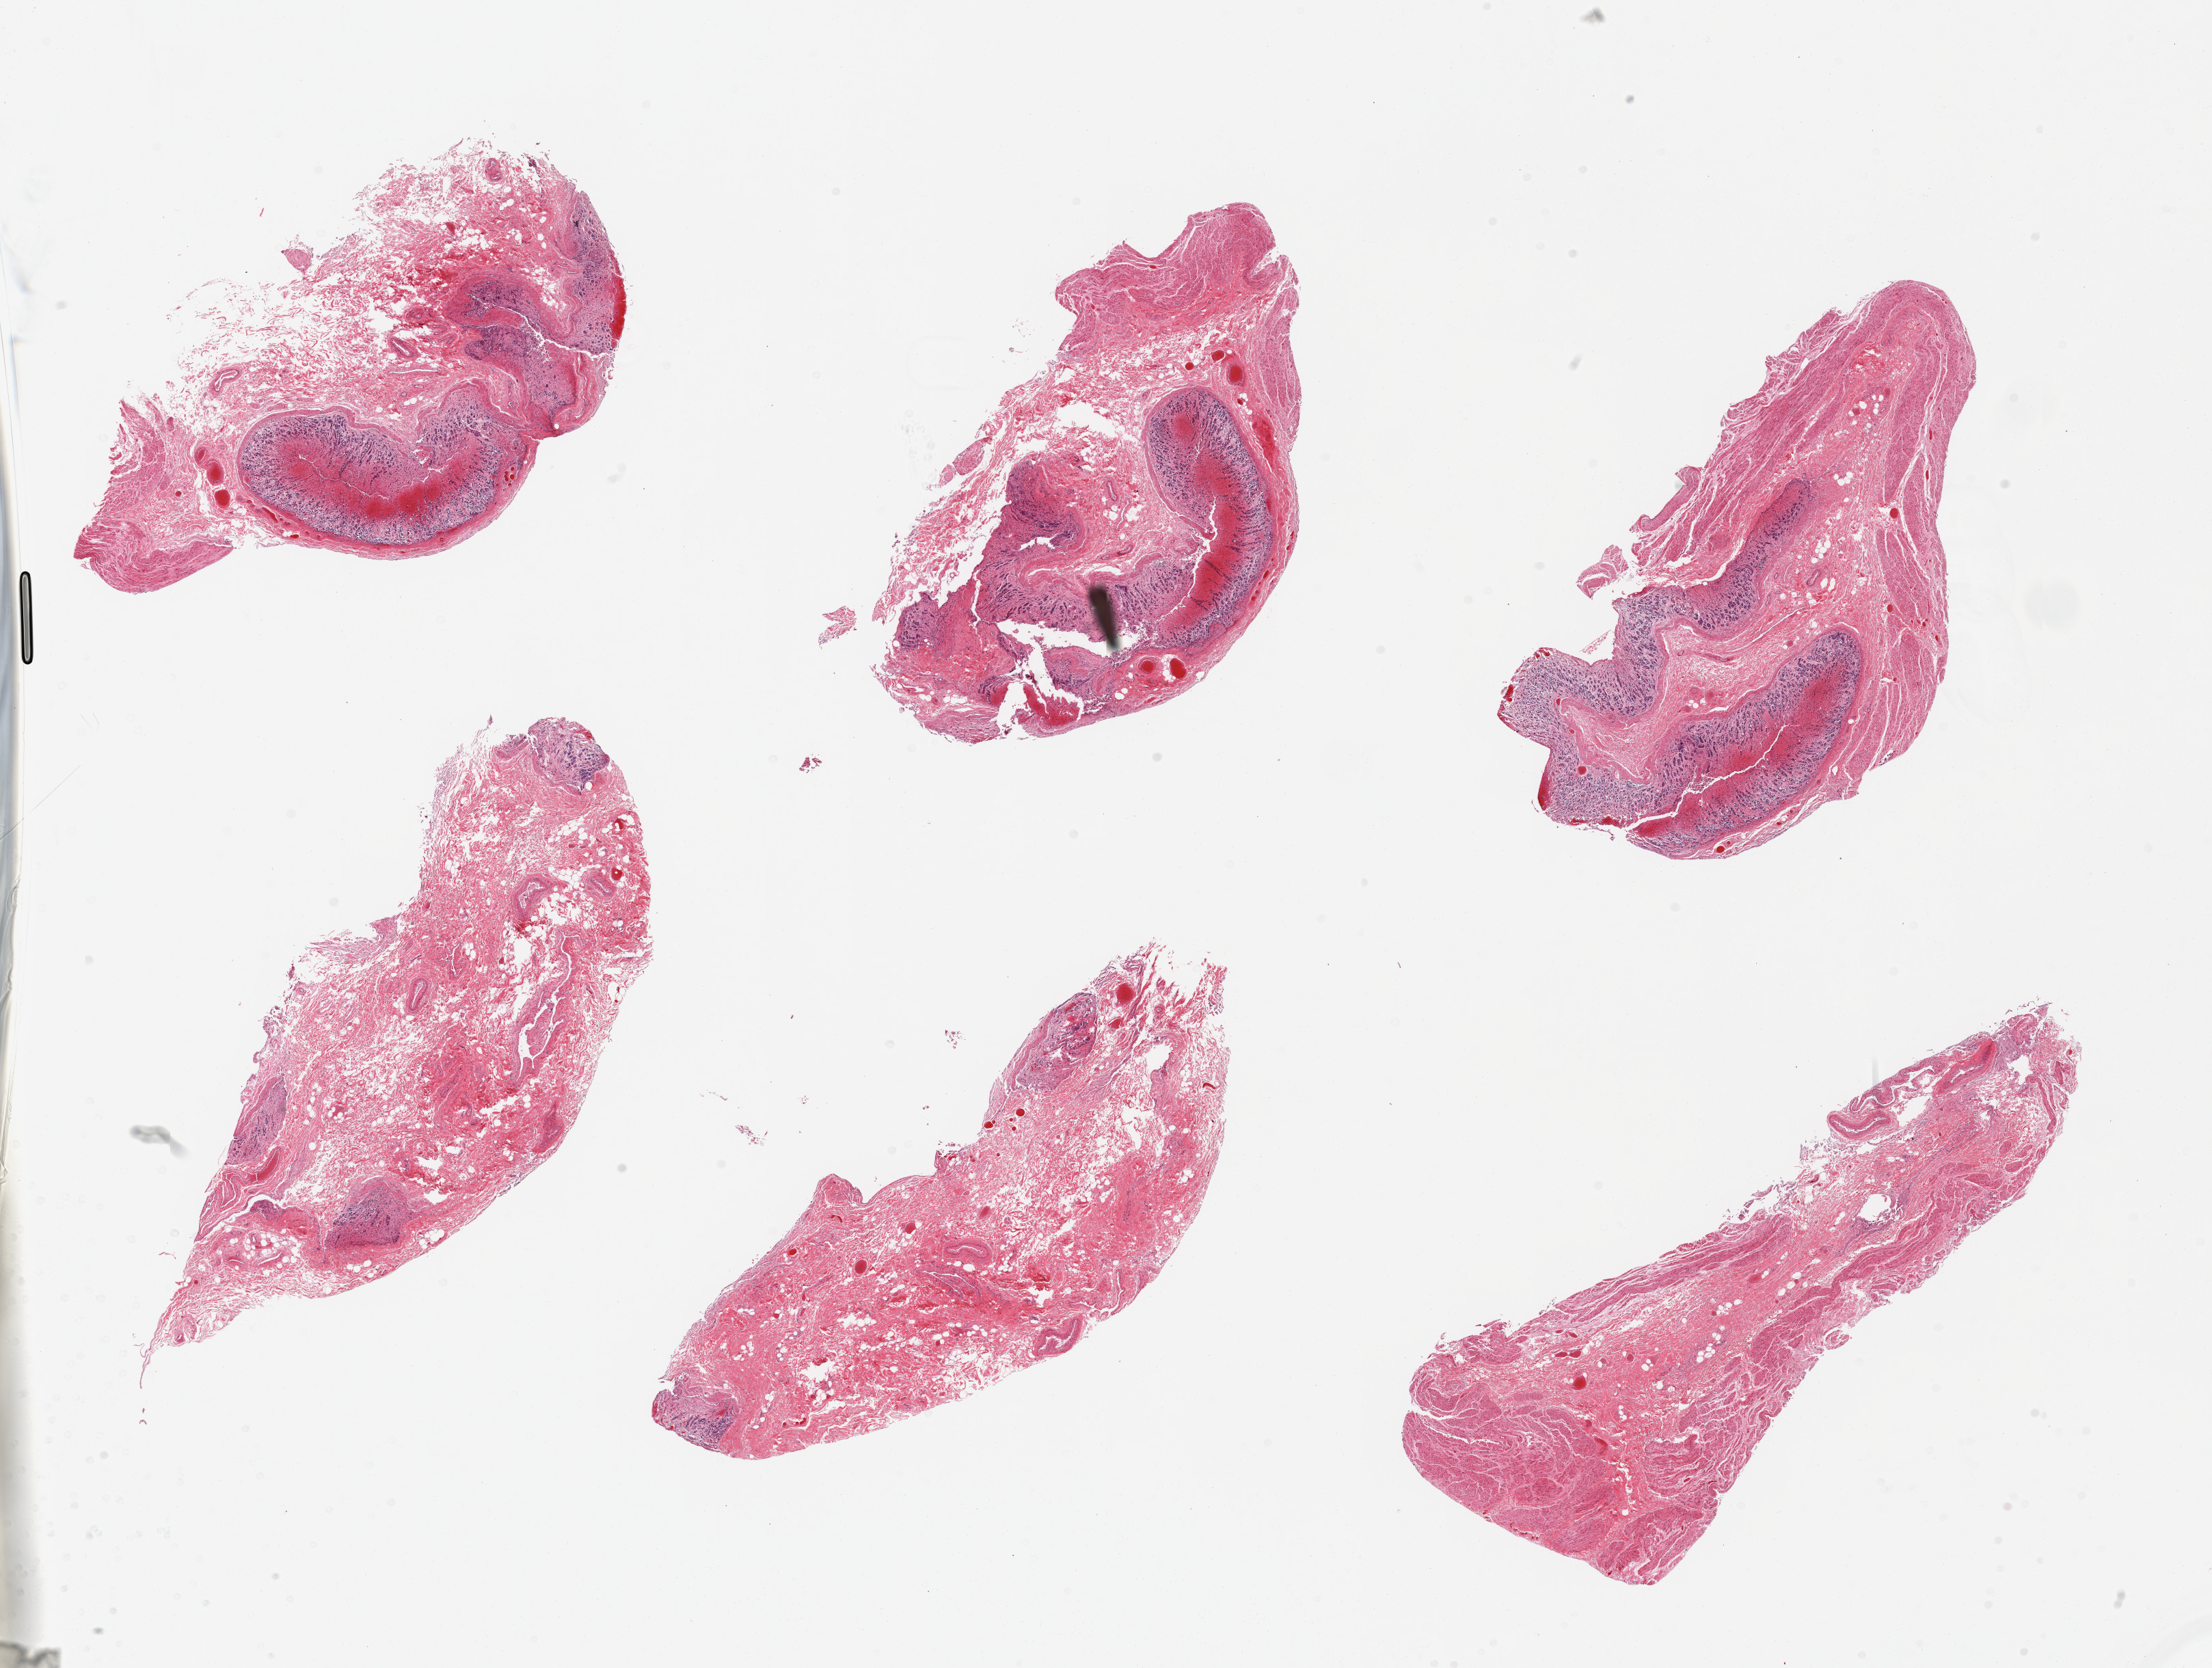
Digitized haematoxylin and eosin-stained section, a low-resolution overview of the entire scanned area, about 25.6 x 19.3 mm. PAXgene-fixed, paraffin-embedded tissue. Sampled site (target tissue): stomach. Tissue donor sample. Male donor.
Reviewer comment on this tissue sample: 6 pieces, a few have up to ~0.6mm mucosal layer but all badly autolyzed.